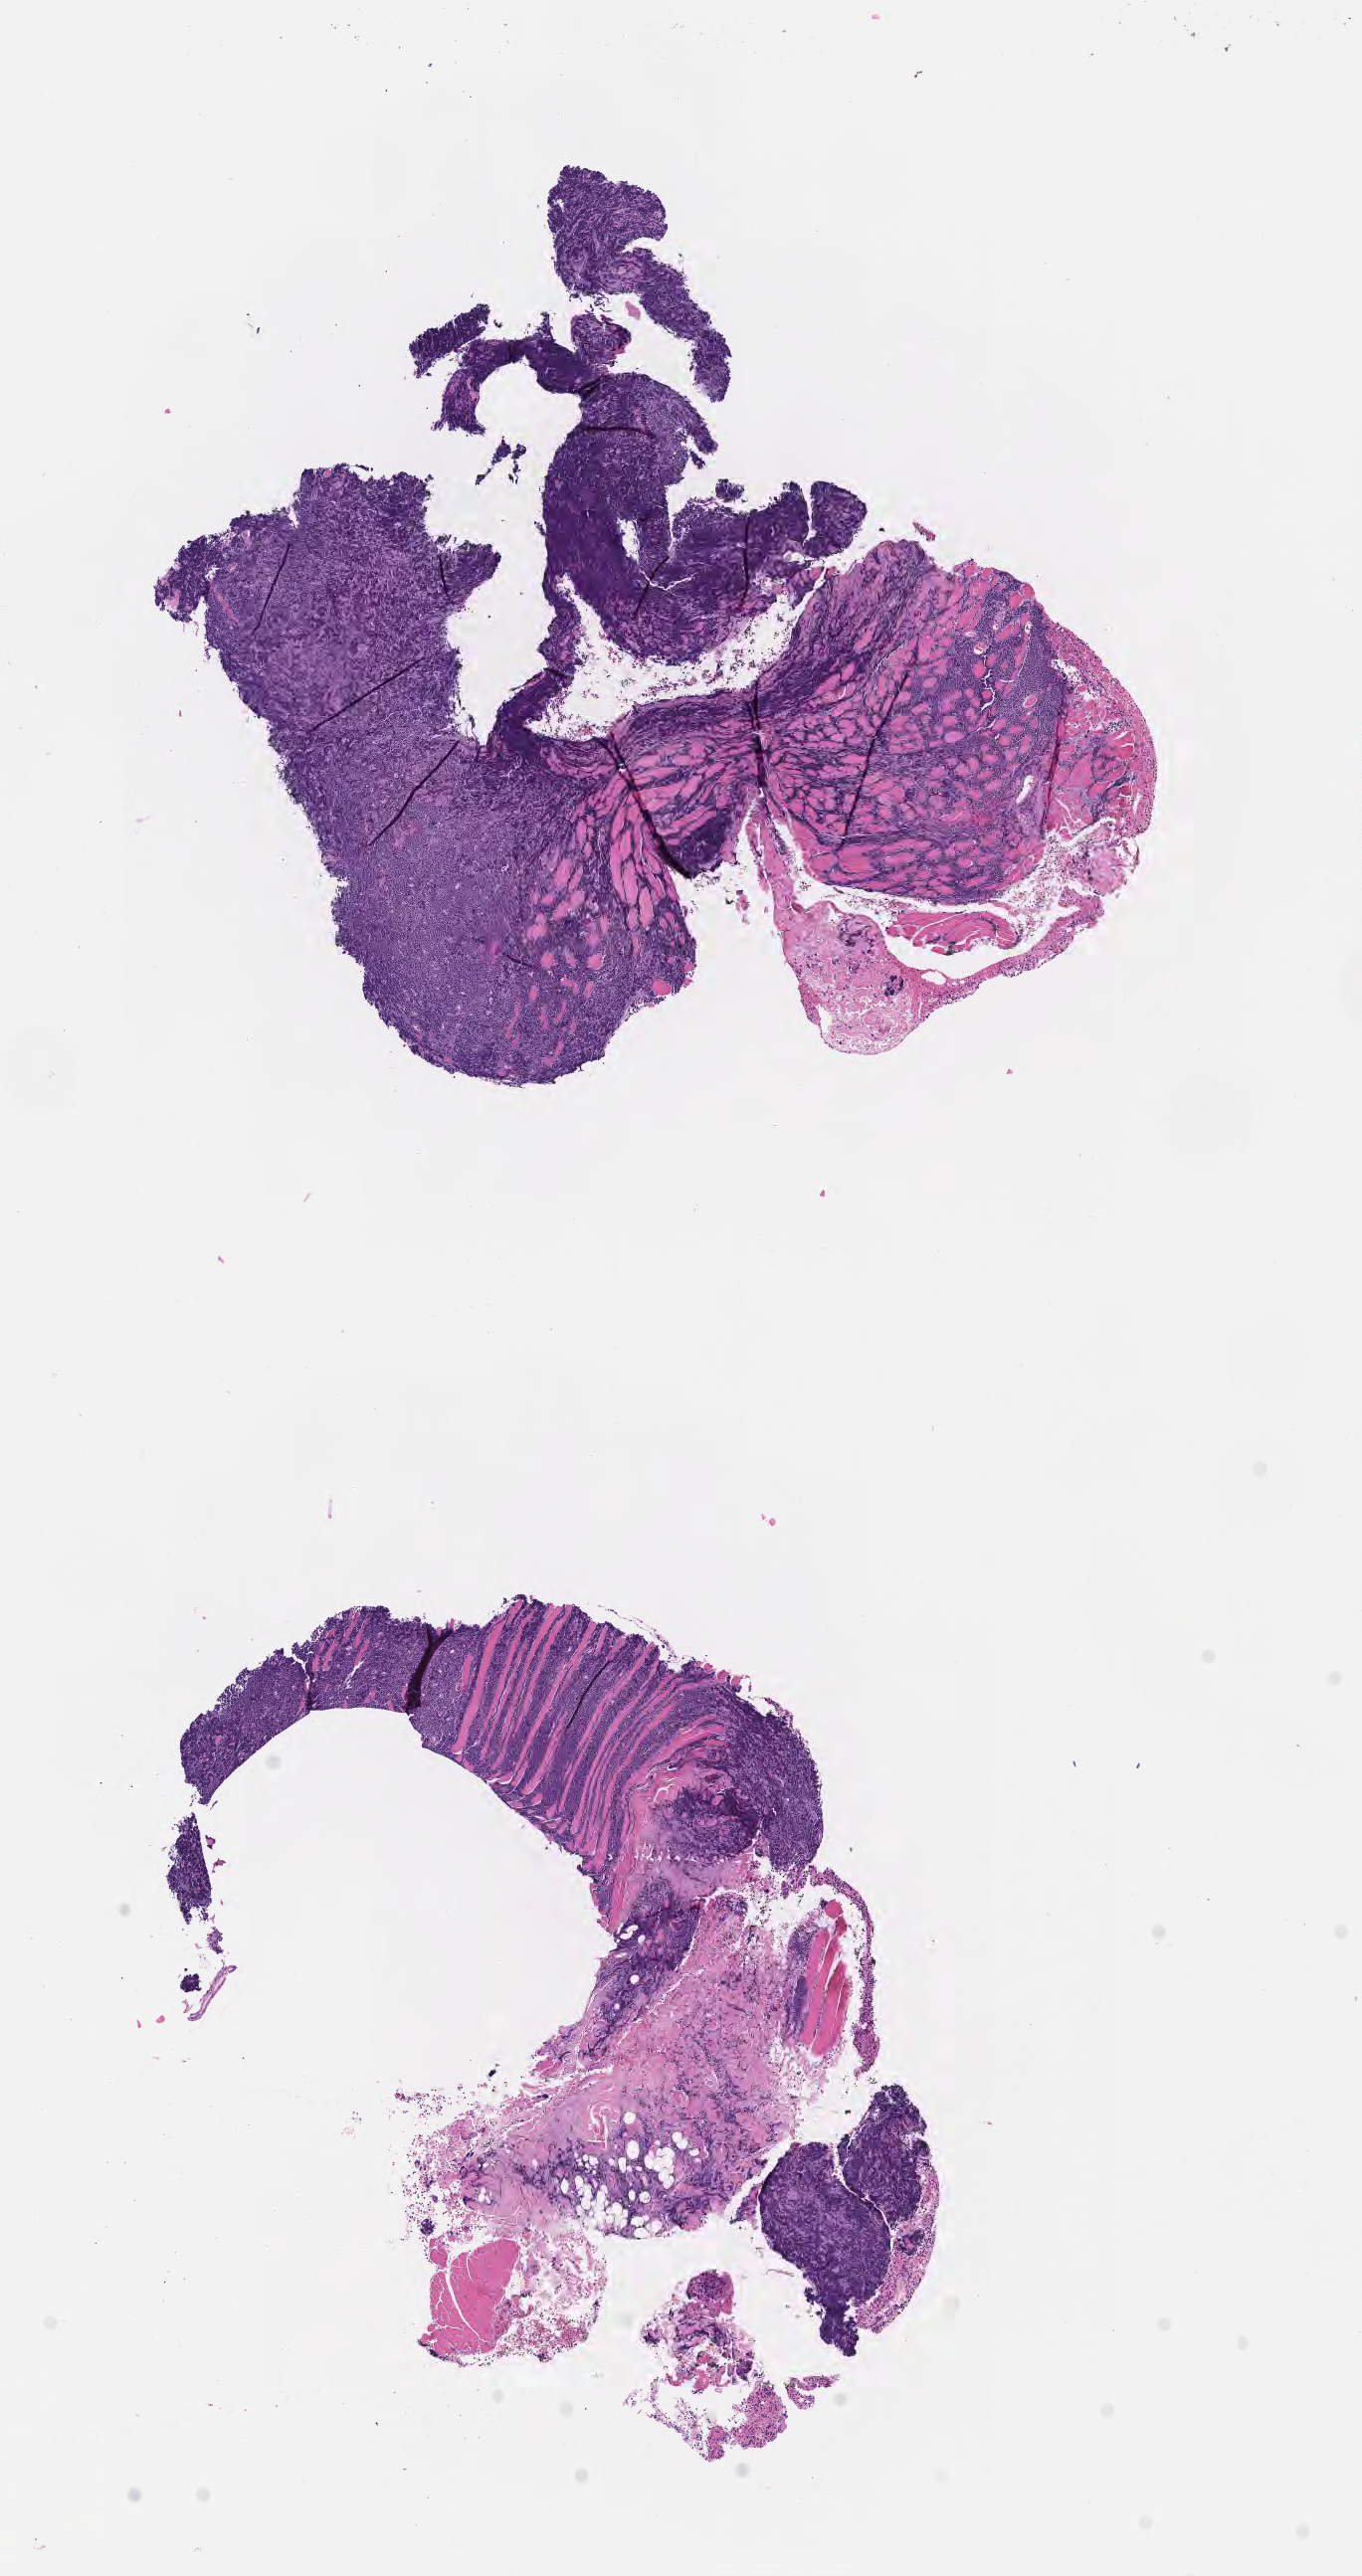
Whole-slide image, haematoxylin and eosin stain — low-resolution overview of the scanned area, about 5.5 x 10.5 mm. Tumor tissue. Anatomic site: lymph node of head and neck. Patient: male, 73 years old.
Diagnosis: Burkitt lymphoma, NOS.